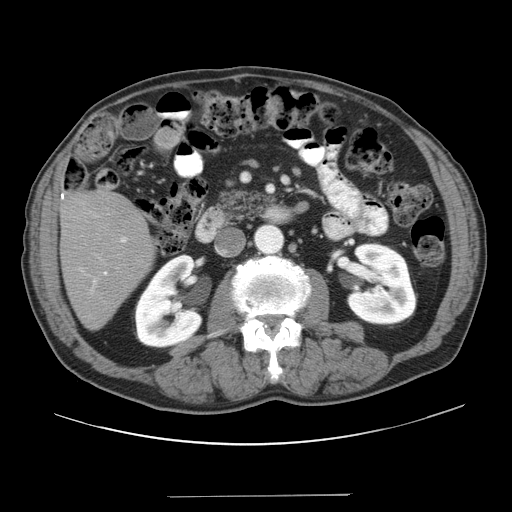
Contrast-enhanced abdominal CT, one axial slice; position 10 of 41 along the scan axis; reconstruction kernel STANDARD; 120 kVp; intravenous contrast given; soft-tissue window (W 400 / L 40 HU); 5 mm slice thickness; 512 × 512 image matrix. Male patient, age 75 years. From the clinical record (not read from this slice): diagnosis: colorectal cancer liver metastases, imaged before liver resection.
Annotated regions visible in this slice (expert manual segmentation):
- liver: bounding box (x1, y1, x2, y2) in pixels: (61, 193, 155, 329)
- planned liver remnant (the part of the liver to remain after resection): (61, 193, 155, 329)
- portal vein (with intrahepatic branches): (91, 237, 128, 292)